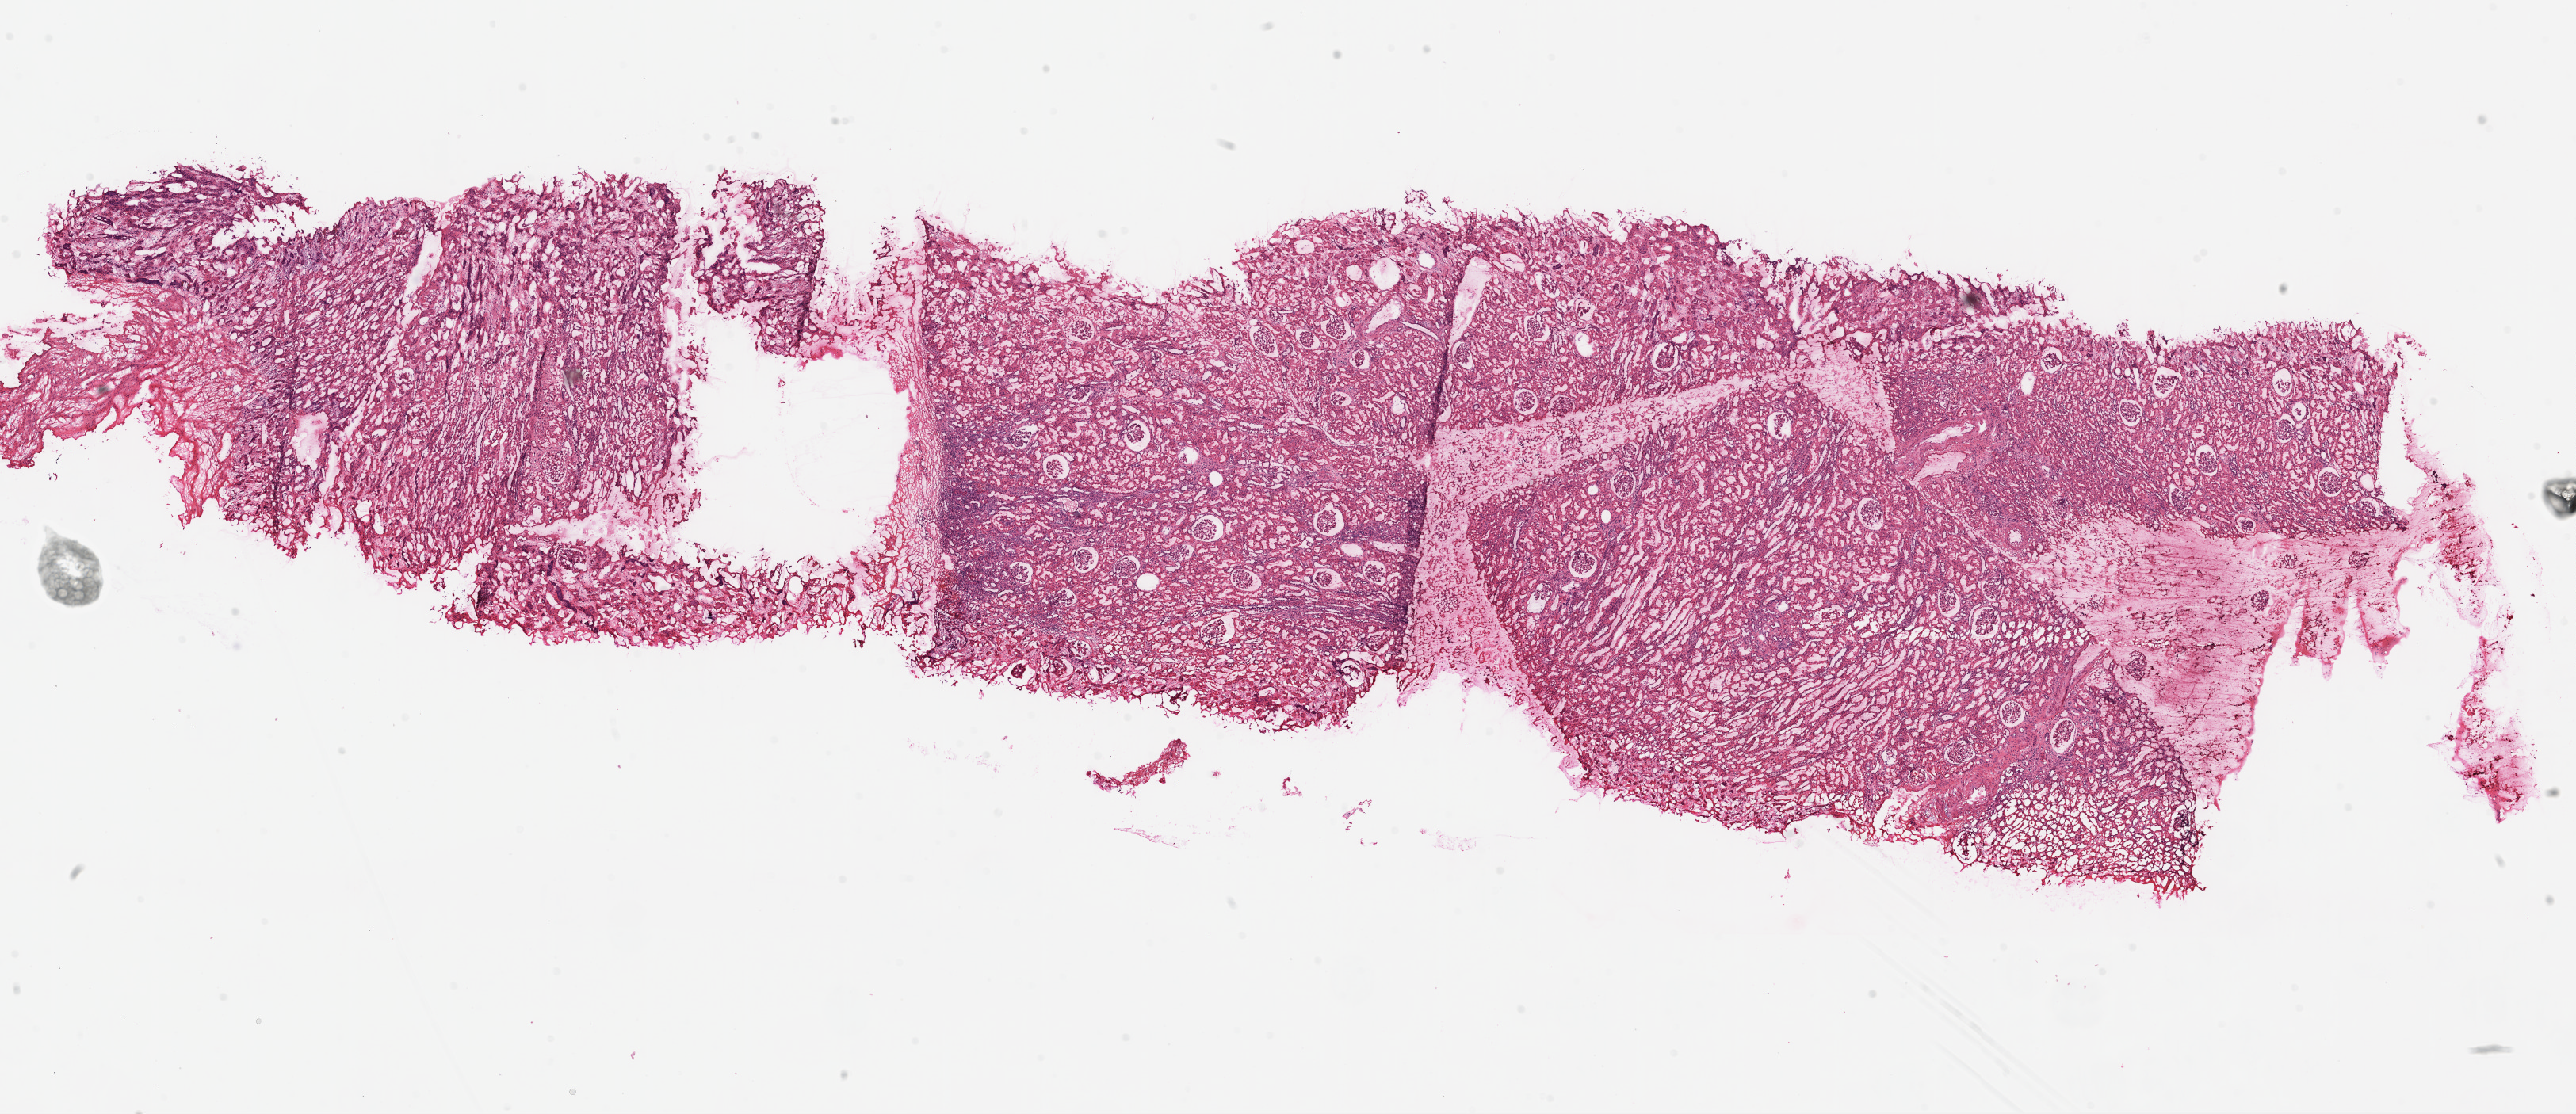
Digitized H&E tissue section (whole slide), whole scanned area (about 26.1 x 11.3 mm, acquisition: 20x scan) shown as a low-resolution overview; frozen section from the top of the tissue portion; kidney, solid tissue normal (non-tumour tissue) sample. Male patient; age at initial diagnosis 49 years.
• this section: solid tissue normal (non-tumour) sample from the same patient
• patient diagnosis: Clear cell adenocarcinoma, NOS